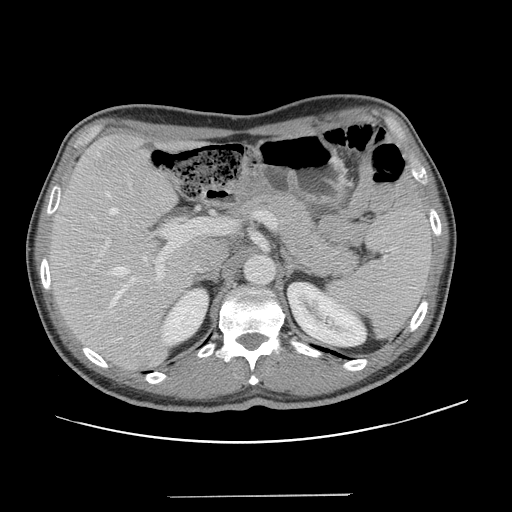
Contrast-enhanced abdominal CT, one axial slice; position 85 of 131 along the scan axis; 120 kVp; intravenous contrast given; soft-tissue window (W 400 / L 40 HU); 512 × 512 image matrix, field of view 403 × 403 mm. Male patient, age 60 years. Case-level facts recorded for this patient, not image findings: diagnosis: colorectal cancer liver metastases, imaged before liver resection.
Annotated regions visible in this slice (outlined manually by an expert reader):
- hepatic veins: bounding box (x1, y1, x2, y2) in pixels: (105, 192, 147, 308)
- liver: (50, 134, 191, 368)
- planned liver remnant (the part of the liver to remain after resection): (50, 135, 191, 355)
- portal vein (with intrahepatic branches): (99, 218, 236, 288)